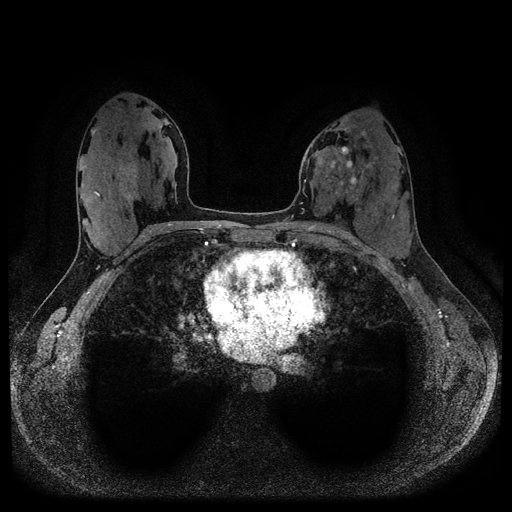
Breast MRI (dynamic contrast-enhanced, multi-phase), one axial slice. Dynamic contrast-enhanced series, time point 2 of 5 at this slice position (early post-contrast). 1.5 T. TE 2.6 ms, TR 5.3 ms. 2 mm slice thickness. 512 × 512 image matrix, field of view 350 × 350 mm. Patient: female, 33 years.
Outlined on this slice (semi-automatic segmentation, software-assisted and operator-edited):
- breast lesion (labelled 'tumour' in the annotation; benign lesions carry a separate 'benign' label): bounding box <327,146,357,188> (left, top, right, bottom; pixels)